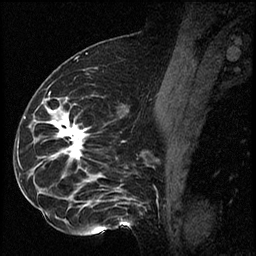
Breast MRI (dynamic contrast-enhanced), one sagittal slice; slice 38 of 60 in the series (ordered by position); dynamic contrast-enhanced series, image 2 of 2 at this slice position (ordered by acquisition); 1.5 T; TE 4.2 ms, TR 17.3 ms; 2 mm slice thickness; 256 × 256 image matrix, field of view 200 × 200 mm. Female patient. Case-level facts recorded for this patient, not image findings: setting: breast cancer imaged before/during neoadjuvant chemotherapy; receptor status: HR-positive, HER2-negative.
Structures marked on this image (semi-automatic segmentation, software-assisted and operator-edited):
- analysis volume of interest (the breast-tissue region the enhancement analysis was run in; not a lesion): bounding box [x1, y1, x2, y2] px = [41, 93, 115, 223]
- tumour enhancement mask (voxels above the 100 % enhancement threshold inside the analysis volume of interest): [56, 118, 84, 158]